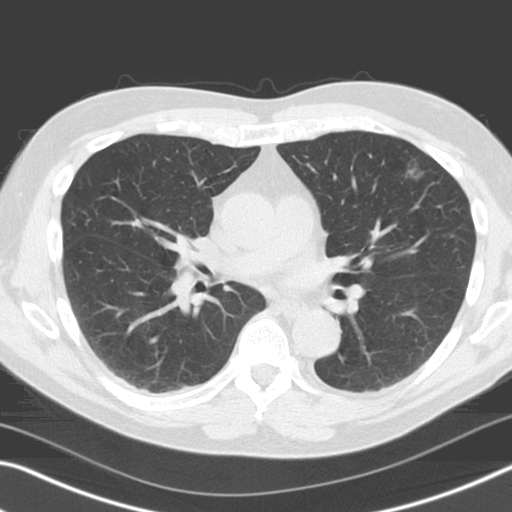
Axial slice from a low-dose chest CT screening exam; baseline screening round; lung window (W 1500 / L -600 HU); 120 kVp; 512 × 512 image matrix, field of view 340 × 340 mm. Male, age 71 years at enrolment. Former smoker at enrolment.
Lesion marked by an expert reader, box from (x=397, y=152) to (x=436, y=189) px. Screening reader's record for this exam (one nodule recorded; not confirmed to be the boxed lesion): non-calcified nodule or mass ≥4 mm, left upper lobe, 11 × 10 mm, poorly defined margins, ground glass attenuation. Official screen result: positive, change unspecified: nodule(s) >= 4 mm or enlarging nodule(s), mass(es), or other non-specific abnormalities suspicious for lung cancer. Participant outcome: lung cancer diagnosed 289 days after this screen — adenocarcinoma, NOS, left upper lobe, moderately differentiated (G2), stage IA (AJCC 6th edition), 11 mm at pathology.